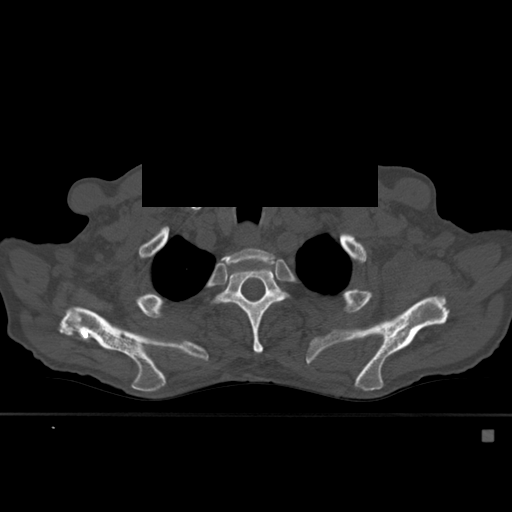
CT including the spine, one axial slice; position 434 of 527 along the scan axis; bone window (W 1800 / L 400 HU); 512 × 512 image matrix, field of view 373 × 373 mm. Patient: male, 78 years. Case-level facts recorded for this patient, not image findings: primary cancer: prostate.
Outlined on this slice (semi-automatically segmented with operator editing):
- T2 vertebra: bounding box <223,248,275,272> (left, top, right, bottom; pixels)
- T3 vertebra: <216,258,286,354>